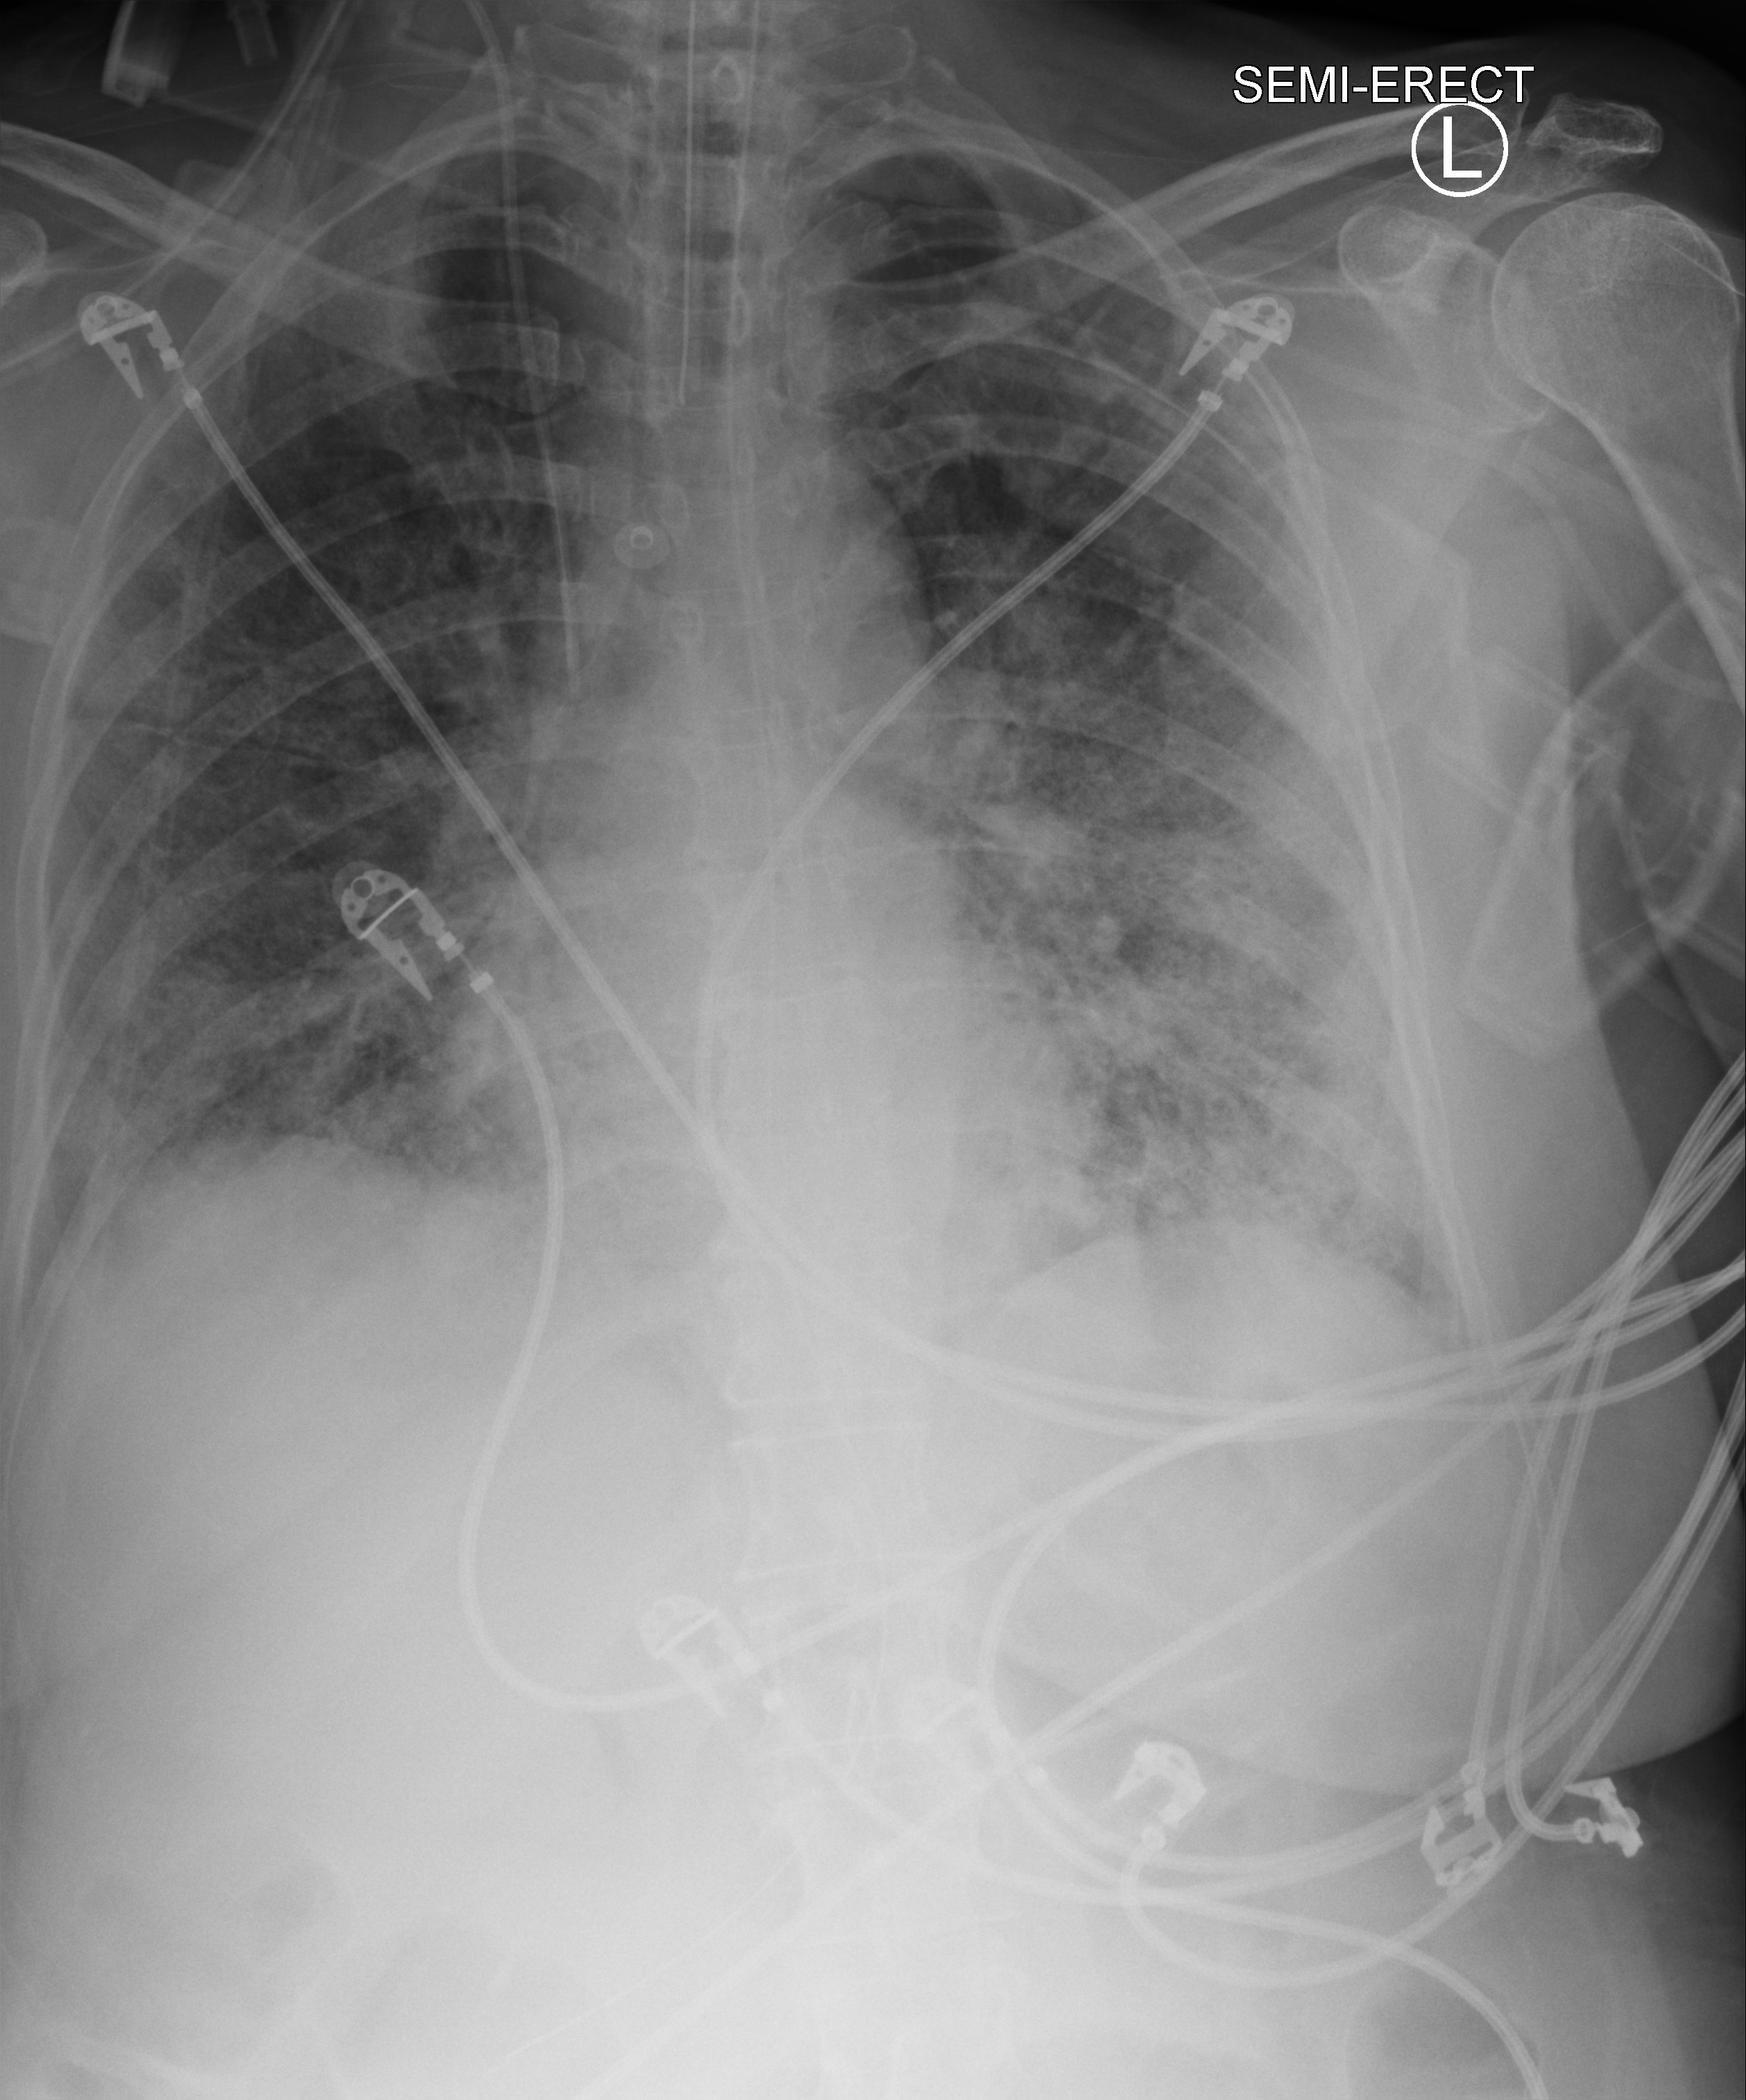
Bedside chest radiograph (computed radiography). Patient hospitalised with COVID-19; female, aged 60–74 years.
Hospital-stay facts (about this admission, not read from this image; timing relative to this image not recorded): other chronic lung disease (admission record): no; mechanically ventilated during this hospital stay: yes; diabetes (admission record): no.